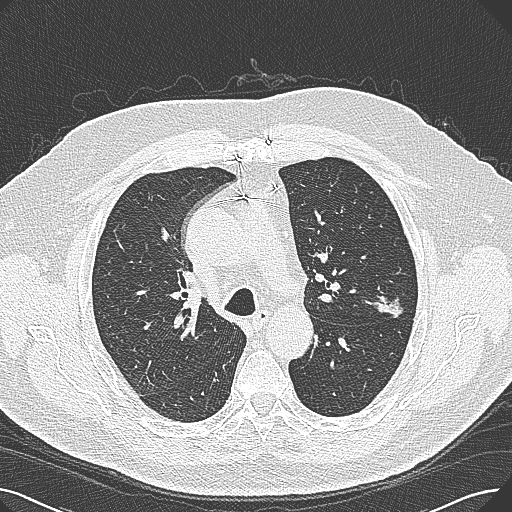
Axial slice from a low-dose chest CT screening exam; first (baseline) screen; lung window (W 1500 / L -600 HU); 1 mm slice thickness; lung (sharp) reconstruction kernel (B80f); 120 kVp; slice 94 of 269 in the series; 512 × 512 image matrix. Male participant, aged 74 years at enrolment. Former smoker at enrolment.
Lesion marked by an expert reader, box from (x=365, y=274) to (x=427, y=326) px. The exam's reader record, not a measurement of the box and not confirmed to be the same lesion: non-calcified nodule or mass ≥4 mm, left upper lobe, 15 × 10 mm, poorly defined margins, soft tissue attenuation. Official screen result: positive, change unspecified: nodule(s) >= 4 mm or enlarging nodule(s), mass(es), or other non-specific abnormalities suspicious for lung cancer. Participant outcome: lung cancer diagnosed 124 days after this screen — adenocarcinoma, NOS, left upper lobe, well differentiated (G1), stage IA (AJCC 6th edition), 26 mm at pathology.